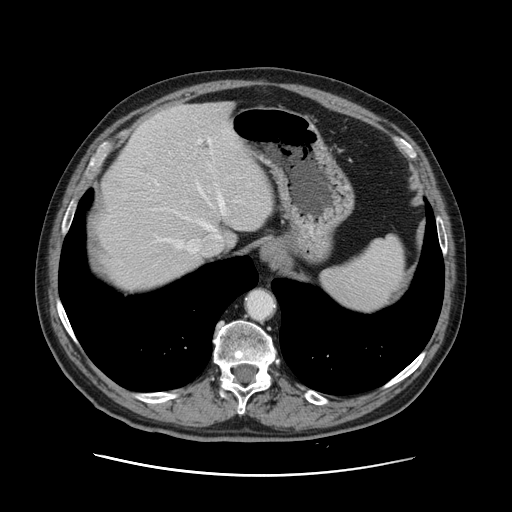
Contrast-enhanced abdominal CT, one axial slice. Position 103 of 141 along the scan axis. 120 kVp. Soft-tissue window (W 400 / L 40 HU). 512 × 512 image matrix. Male patient, age 72 years. Case-level facts recorded for this patient, not image findings: diagnosis: colorectal cancer liver metastases, imaged before liver resection; multiple liver metastases: yes; largest metastasis: 5.4 cm; chemotherapy before resection: yes.
Outlined on this slice (manually delineated by an expert):
- hepatic veins: bounding box (x1, y1, x2, y2) in pixels: (157, 139, 224, 253)
- liver: (96, 102, 274, 293)
- planned liver remnant (the part of the liver to remain after resection): (108, 102, 274, 293)
- portal vein (with intrahepatic branches): (198, 139, 238, 202)